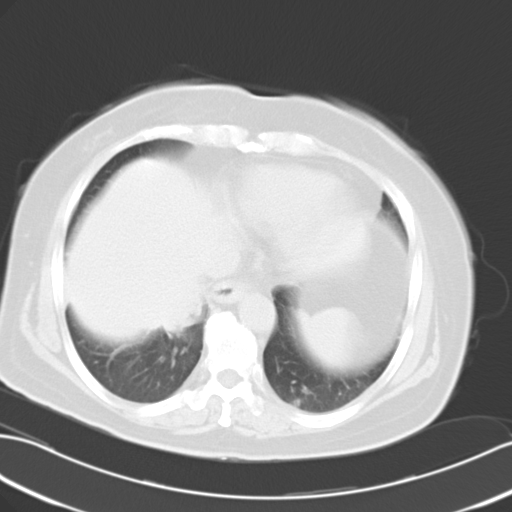
Chest CT, one axial slice; slice 8 of 24 in the series (ordered by position); reconstruction kernel B40f; lung window (W 1500 / L -600 HU); 10 mm slice thickness; 512 × 512 image matrix, field of view 353 × 353 mm. Patient: female, 63 years. Case-level facts recorded for this patient, not image findings: clinical TNM (as recorded): T3 N0 M0.
Outlined on this slice (rectangle marked by the reading radiologist):
- lung tumour (recorded histology: adenocarcinoma): bounding box [x1, y1, x2, y2] px = [156, 284, 203, 337]